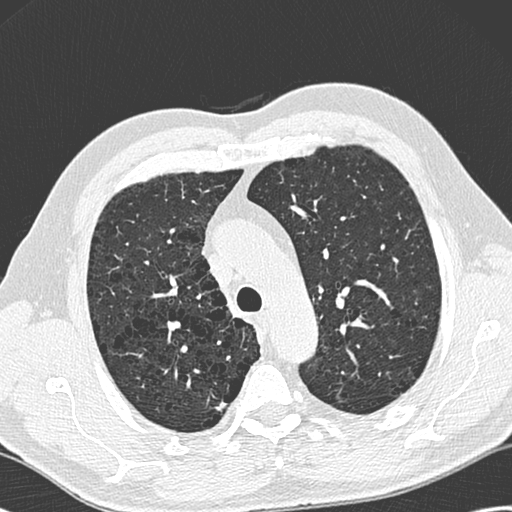
Chest CT (low-dose screening protocol), one axial image. Baseline annual screen. Lung window (W 1500 / L -600 HU). Lung (sharp) reconstruction kernel (D). 120 kVp. Slice 65 of 258 in the series. Male participant, aged 68 years at enrolment.
Expert reader's lesion annotation, box from (x=204, y=392) to (x=243, y=421) px. Screening reader's record for this exam: no non-calcified nodule ≥4 mm recorded. Lung cancer was diagnosed 777 days after this screen: adenocarcinoma, NOS, right upper lobe, well differentiated (G1), stage IB (AJCC 6th edition), 15 mm at pathology.